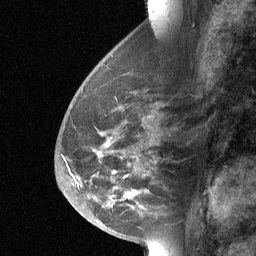
Breast MRI (dynamic contrast-enhanced), one sagittal slice; dynamic contrast-enhanced study with each time point stored as its own series, time point 2 of 3 at this slice position (early post-contrast, ordered by acquisition time); 1.5 T; TE 4.8 ms, TR 27 ms; 2 mm slice thickness; 256 × 256 image matrix, field of view 180 × 180 mm. Female patient, age 56 years. Case-level facts recorded for this patient, not image findings: setting: breast cancer imaged before/during neoadjuvant chemotherapy; receptor status: HER2-positive.
Outlined on this slice (semi-automatic segmentation, software-assisted and operator-edited):
- analysis volume of interest (the breast-tissue region the enhancement analysis was run in; not a lesion): box from (x=68, y=83) to (x=165, y=214) px
- tumour enhancement mask (voxels above the 90 % enhancement threshold inside the analysis volume of interest): (x=106, y=142)–(x=115, y=172)